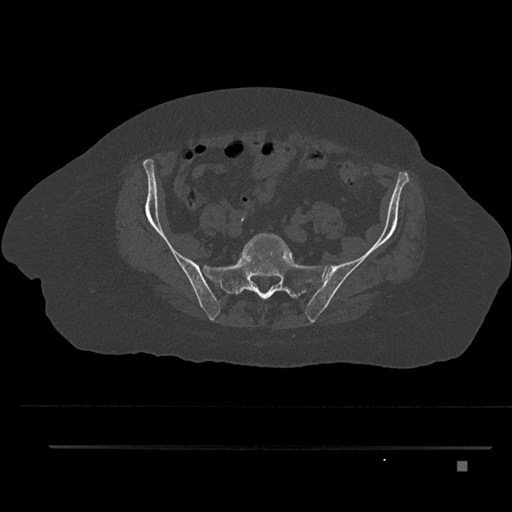
CT including the spine, one axial slice; slice 9 of 797 in the series (ordered by position); bone window (W 1800 / L 400 HU); 512 × 512 image matrix, field of view 437 × 437 mm. Female patient, age 76 years. Case-level facts recorded for this patient, not image findings: primary cancer: lung; vertebrae with lytic lesions (as recorded): T11, L3.
Outlined on this slice (semi-automatic segmentation, software-assisted and operator-edited):
- L5 vertebra: bounding box <243,232,292,259> (left, top, right, bottom; pixels)